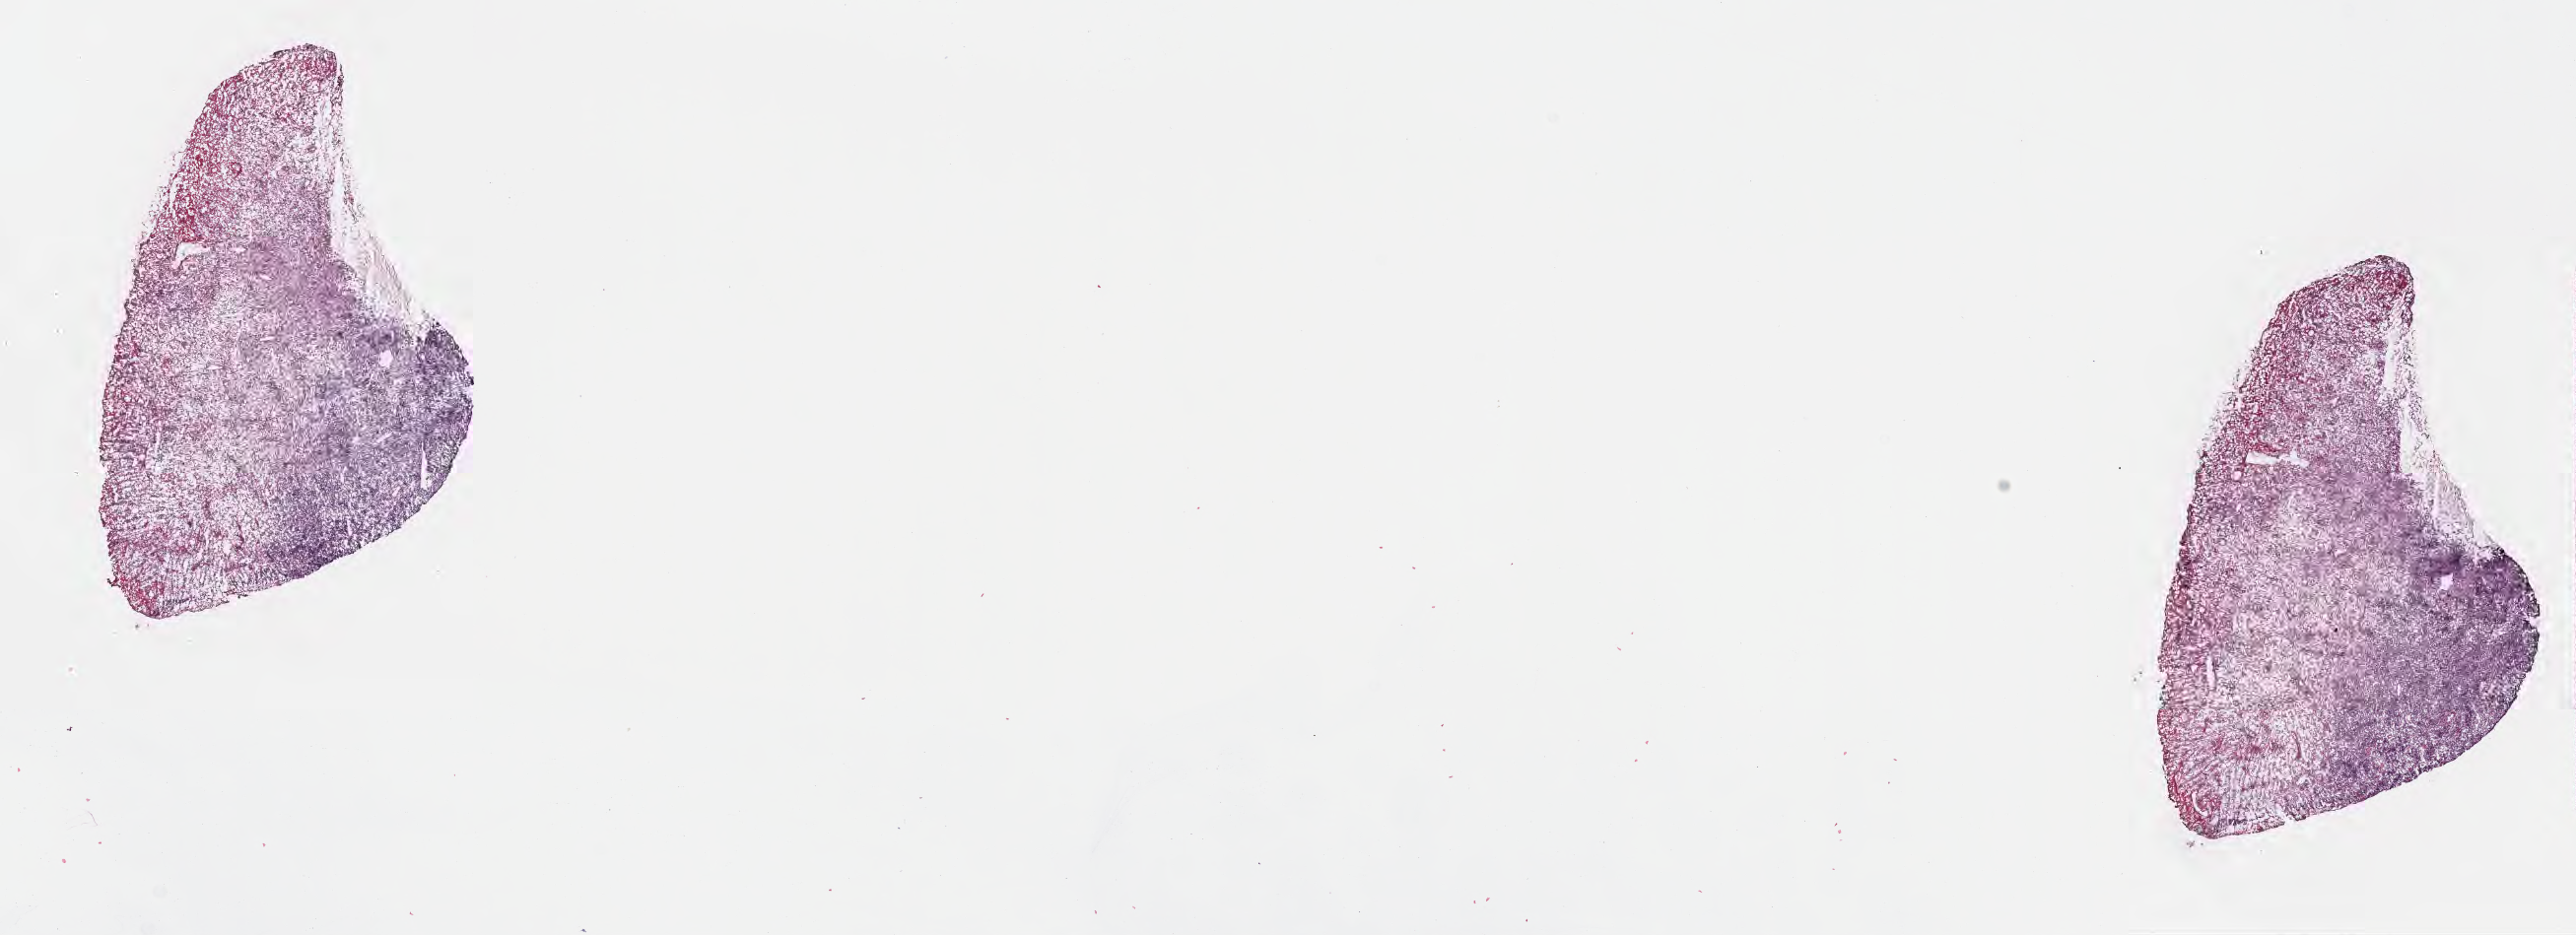
Whole-slide image, haematoxylin and eosin stain, shown as a low-resolution overview of the whole scanned area (about 21.1 x 7.7 mm), cryosection, specimen: primary tumor, anatomic site: mandible. Patient: female, age at initial diagnosis 7 years. Pathologist review of this section (percent, as recorded): tumor cells 30%, tumor nuclei 40%, stromal cells 70%, necrosis 0%, normal cells 0%. Inflammatory infiltration, as recorded: lymphocyte infiltration 50%, monocyte infiltration 30%, neutrophil infiltration 10%.
Ann Arbor stage (patient): Stage IV. Section: bottom of the tissue portion. Histologic diagnosis: Burkitt lymphoma, NOS.